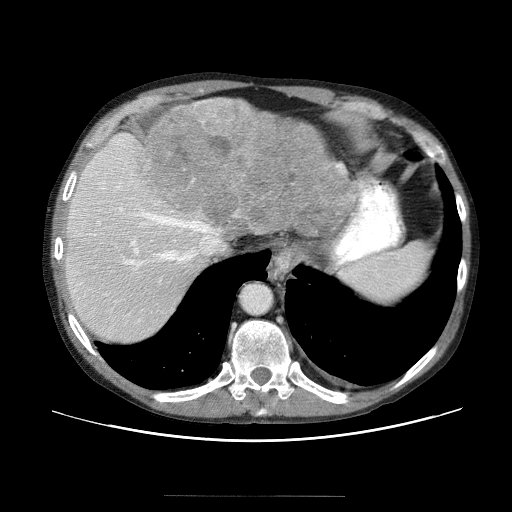
Contrast-enhanced abdominal CT (liver protocol), one axial slice. Position 49 of 69 along the scan axis. 120 kVp. Soft-tissue window (W 400 / L 40 HU). 2.5 mm slice thickness. 512 × 512 image matrix, field of view 380 × 380 mm. Case-level facts recorded for this patient, not image findings: diagnosis: hepatocellular carcinoma (patient treated with transarterial chemoembolisation; whether this scan precedes or follows treatment is not stated here); TNM stage (as recorded): Stage-IVB; Child-Pugh class: B; tumour differentiation: poorly differentiated; tumour nodularity: multinodular.
Outlined on this slice (semi-automatically segmented with operator editing):
- liver parenchyma outside the tumour (the mass and vessels are separate outlines, so this box may not span the whole liver): bounding box <62,120,352,348> (left, top, right, bottom; pixels)
- mass: <144,97,362,247>
- liver vessels: <97,188,172,318>